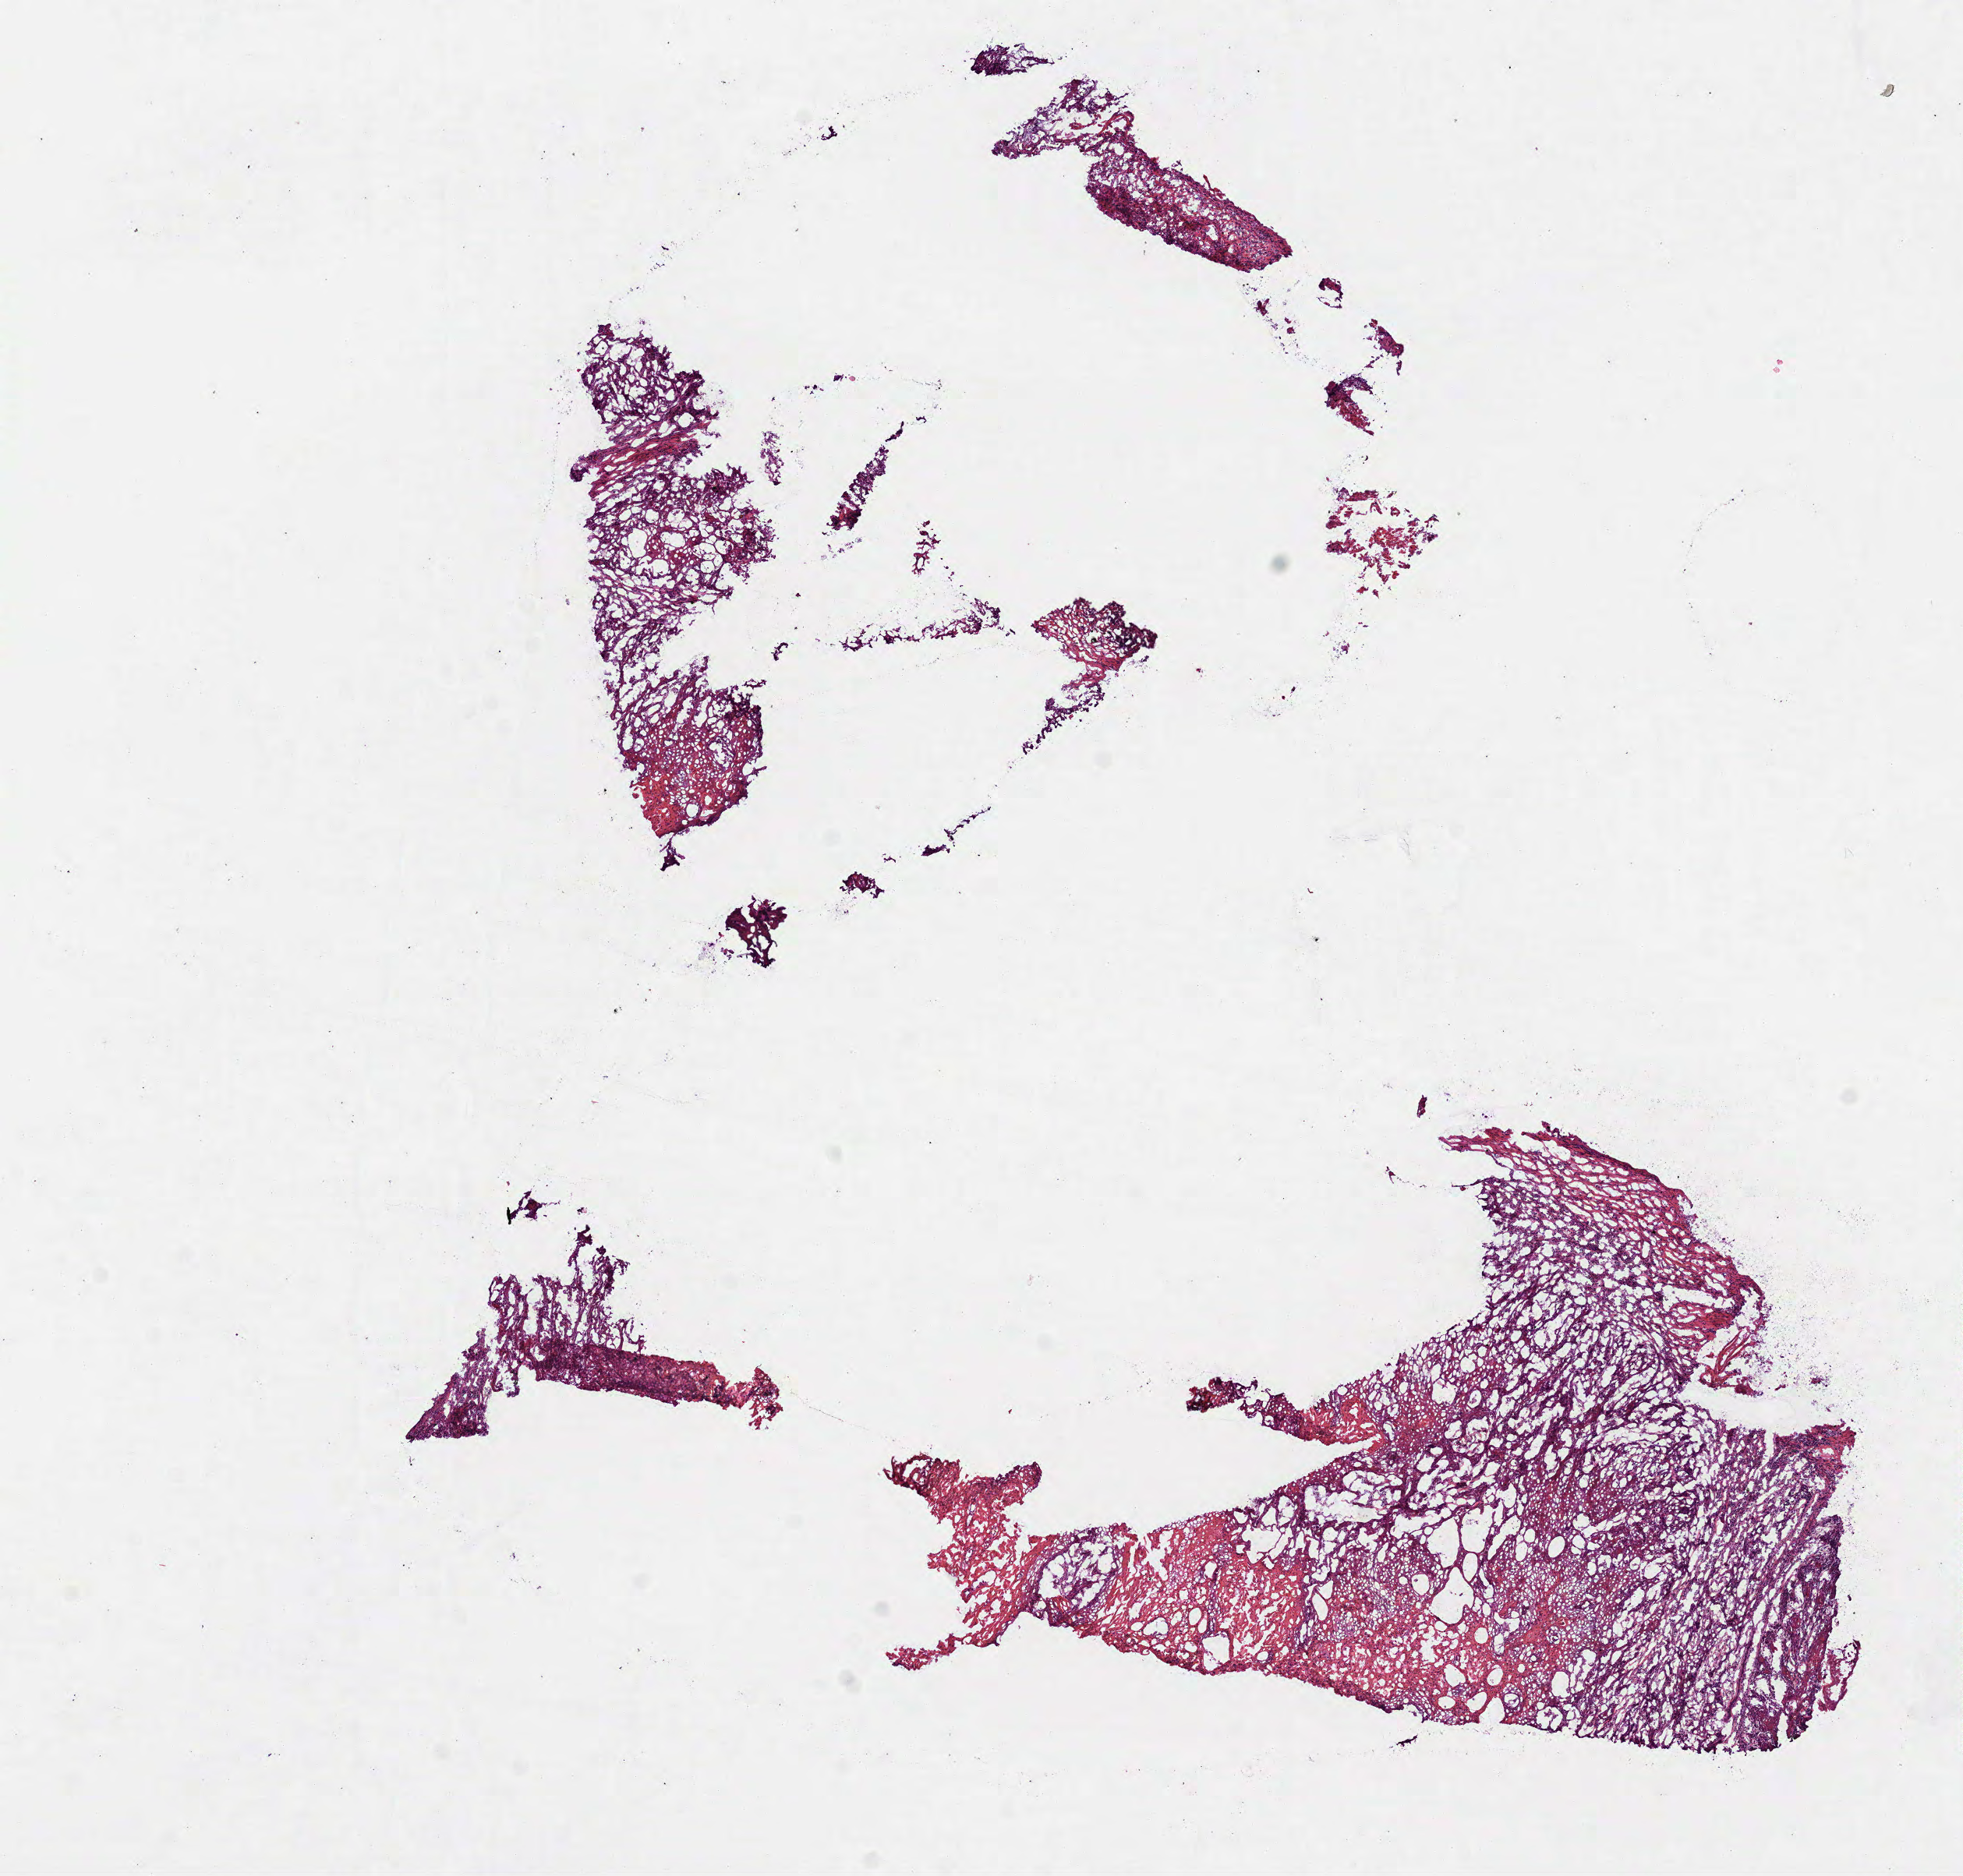
H&E whole-slide image — a low-resolution overview of the entire scanned area, about 10.2 x 9.7 mm; frozen section from the bottom of the tissue portion; head and neck, primary tumour sample. Patient: male, age at initial diagnosis 59 years. Histologic grade: G2 (moderately differentiated). Pathologist review of this section (percent, as recorded): tumour cells 100%, tumour nuclei 80%, normal cells 0%, stromal cells 0%, necrosis 0%. Inflammatory infiltration, as recorded: lymphocyte infiltration 5%, monocyte infiltration 0%, neutrophil infiltration 10%.
- lymph nodes positive (case pathology): 0 of 22 examined
- pathologic diagnosis: Squamous cell carcinoma, NOS (tongue, NOS)
- TNM: T4a NX
- AJCC pathologic stage: IVA (7th edition)